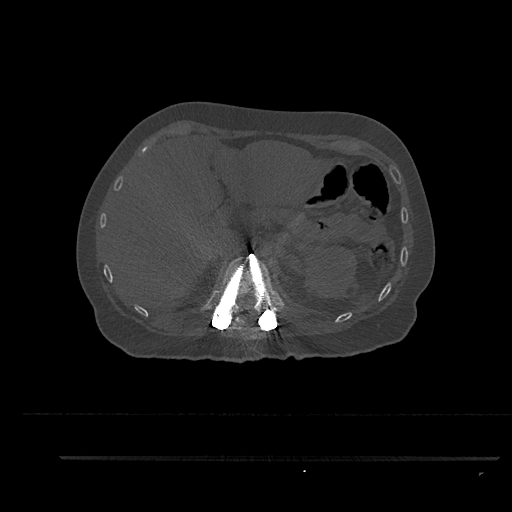
CT including the spine, one axial slice; slice 276 of 797 in the series (ordered by position); reconstruction kernel Br40s/3; bone window (W 1800 / L 400 HU); 0.5 mm slice thickness; 512 × 512 image matrix, field of view 408 × 408 mm. Female patient, age 44 years. From the clinical record (not read from this slice): primary cancer: renal.
Annotated regions visible in this slice (semi-automatic segmentation, software-assisted and operator-edited):
- T11 vertebra: box from (x=232, y=317) to (x=252, y=340) px
- T12 vertebra: (x=213, y=256)–(x=282, y=319)